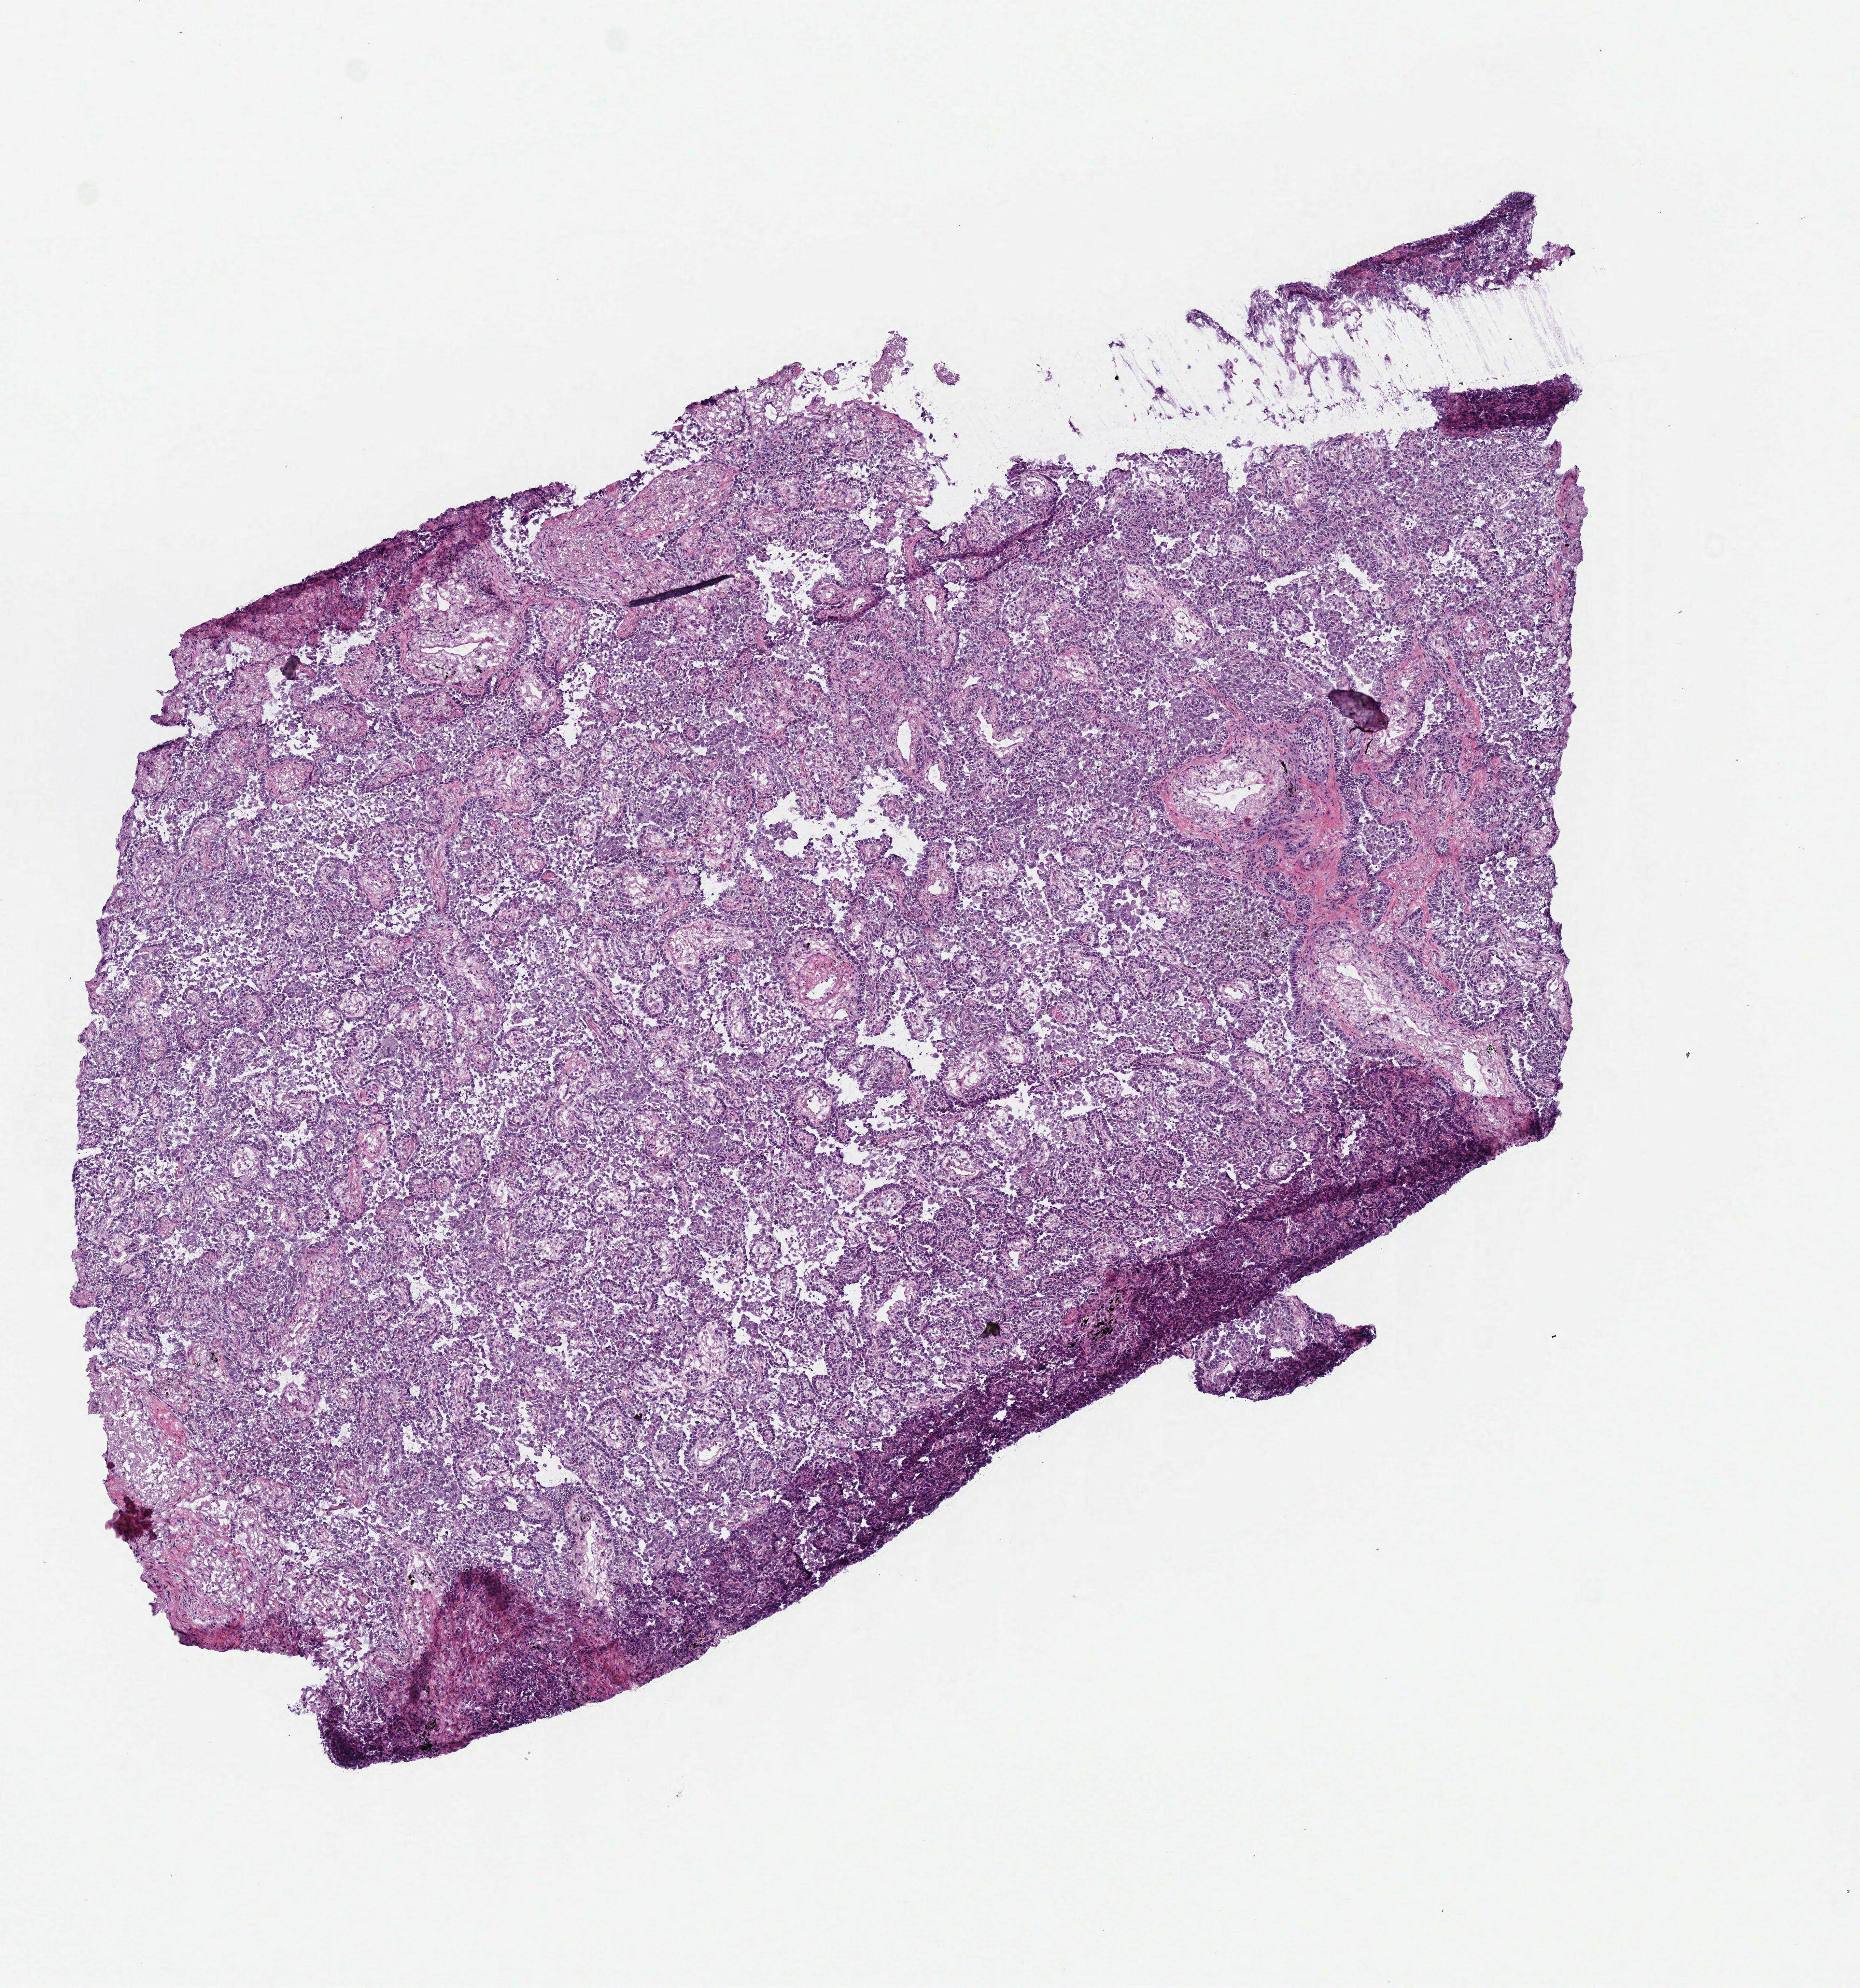
H&E-stained whole-slide image — a low-resolution overview of the entire scanned area, about 5.6 x 6.0 mm (slide scanned at 40x), frozen section from the top of the tissue portion, sample: primary tumour, lung. Patient sex: male. Composition of this section per pathologist review: tumour cells 100%, tumour nuclei 80%, normal cells 0%, stromal cells 0%, necrosis 0%. Infiltration values recorded for this section: lymphocyte infiltration 10%, monocyte infiltration 2%, neutrophil infiltration 0%.
* TNM: T2 N0 M0
* pathologic diagnosis: Adenocarcinoma, NOS
* AJCC pathologic stage: IB (6th edition)
* laterality: right